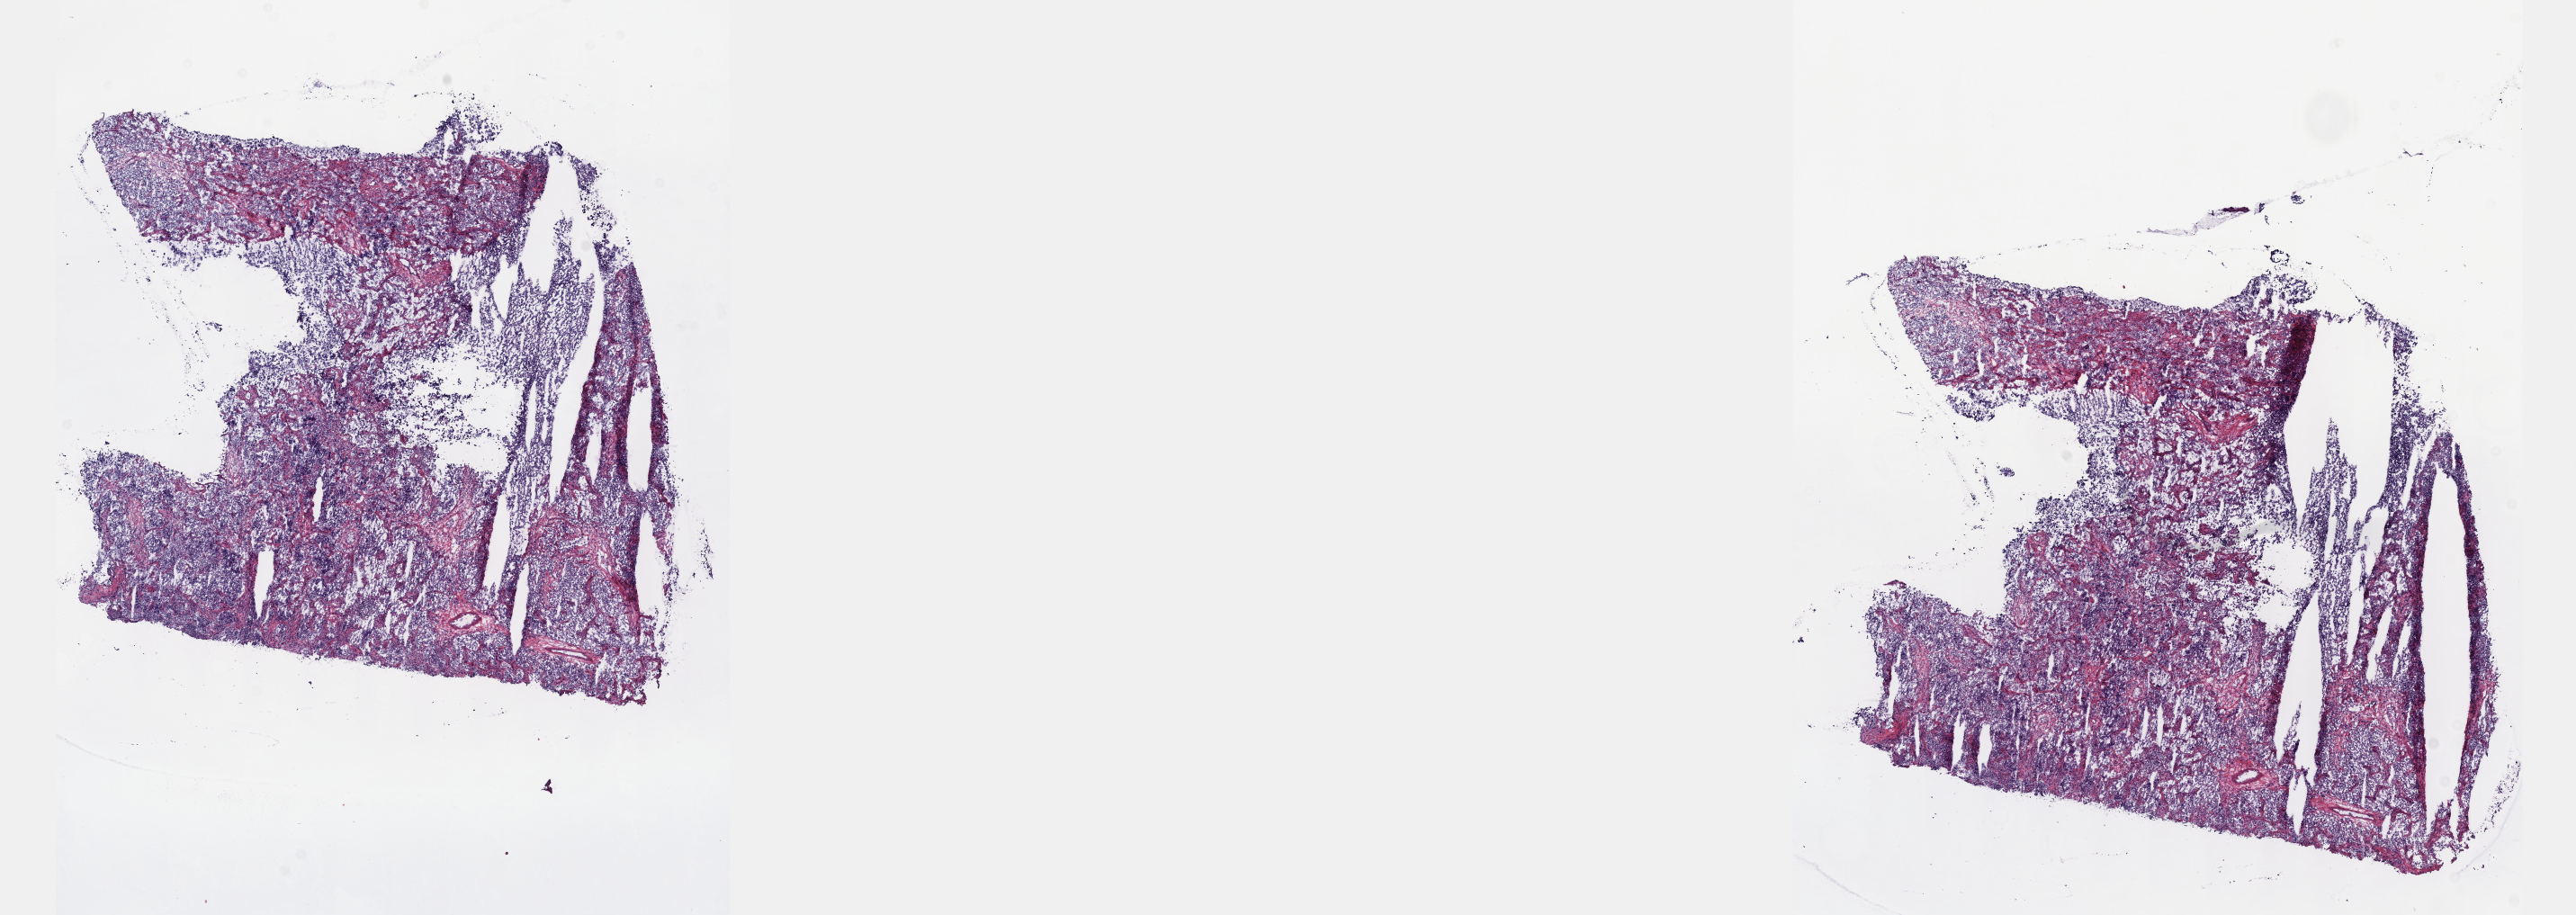
H&E-stained whole-slide image — a low-resolution overview of the entire scanned area, about 23.1 x 8.2 mm (from a 40x scan). Frozen section from the top of the tissue portion. Primary tumour sample from the testis. Patient: male, age at initial diagnosis 52 years. Pathologist review of this section (percent, as recorded): tumour cells 80%, tumour nuclei 70%, normal cells 0%, stromal cells 20%, necrosis 0%. Inflammatory infiltration, as recorded: lymphocyte infiltration 90%, monocyte infiltration 0%, neutrophil infiltration 0%.
AJCC pathologic stage: IB (6th edition). Histologic diagnosis: Seminoma, NOS. Laterality: left.